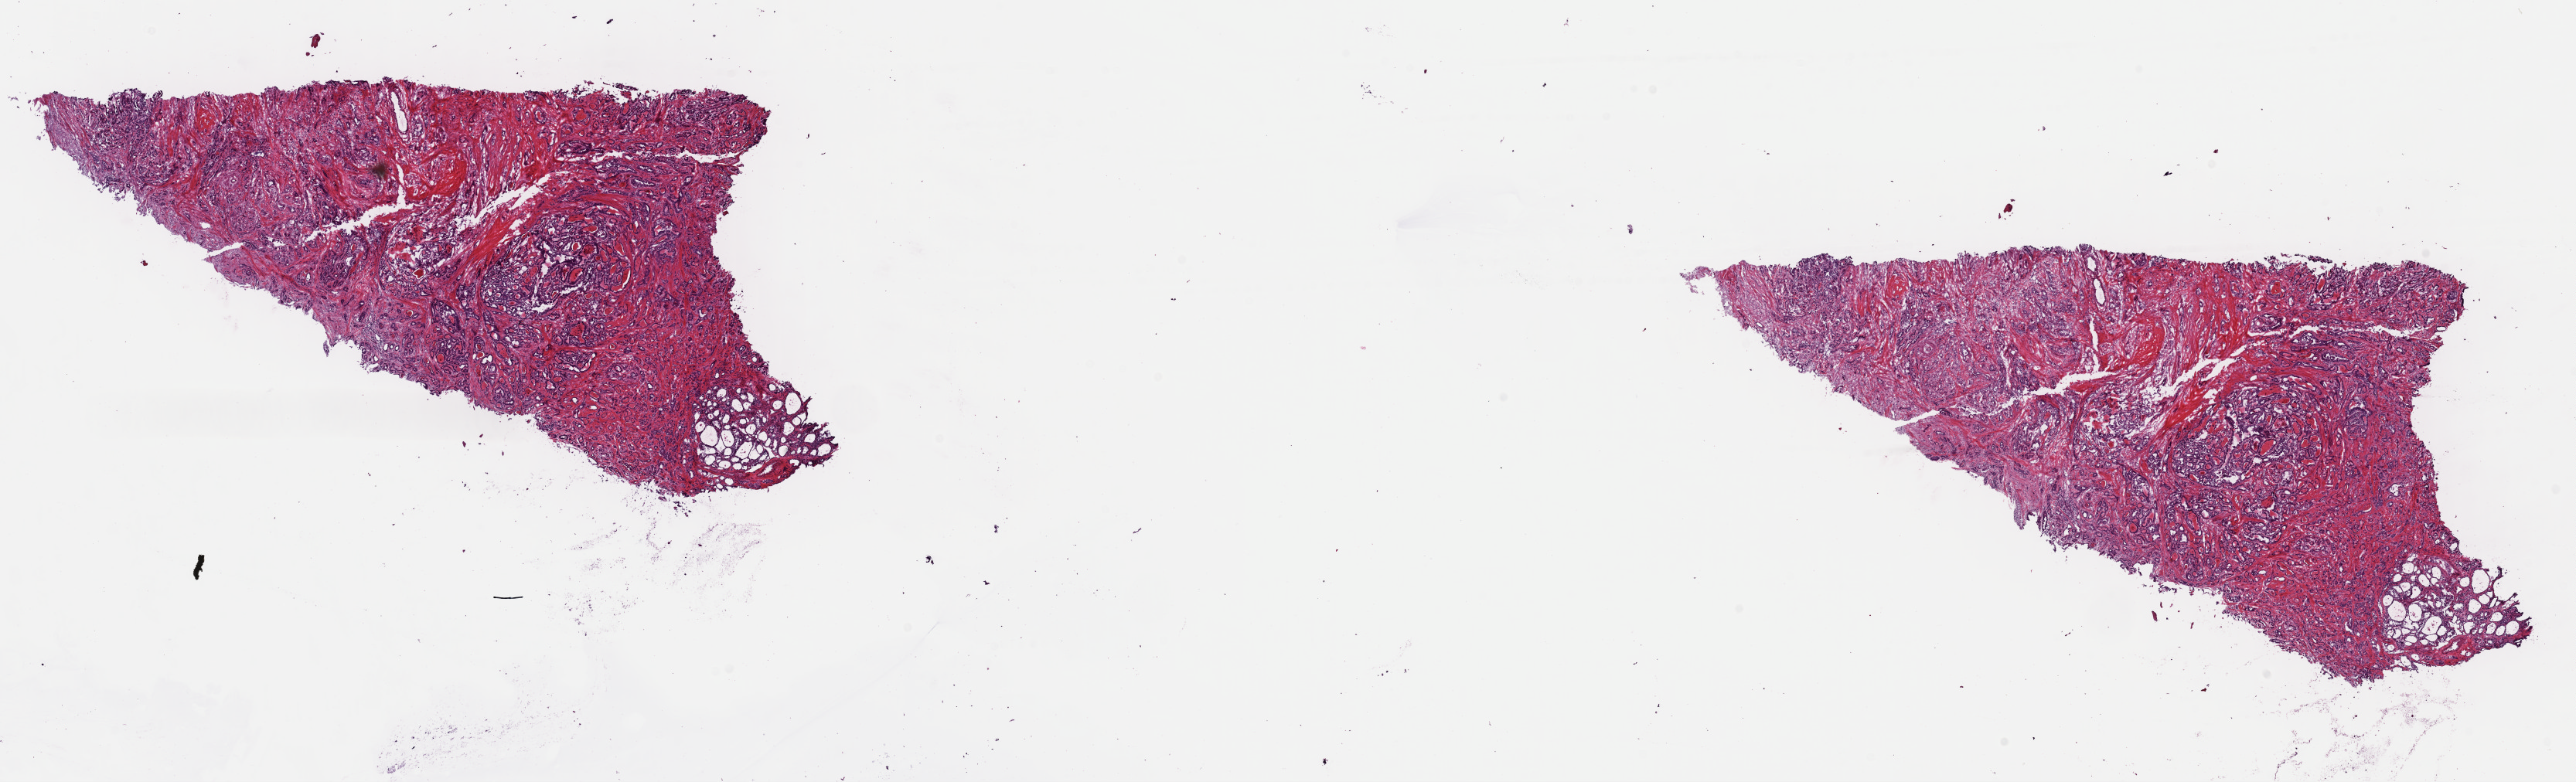
Hematoxylin and eosin (H&E) stained whole-slide image, shown as a low-resolution overview of the whole scanned area (about 26.3 x 8.0 mm, acquisition: 40x scan); frozen section from the top of the tissue portion; thyroid, primary tumour sample. Female patient; age at initial diagnosis 56 years. Slide review estimates, as recorded: tumour cells 95%, tumour nuclei 70%, normal cells 5%, stromal cells 0%, necrosis 0%. Inflammatory infiltration, as recorded: lymphocyte infiltration 0%, monocyte infiltration 0%, neutrophil infiltration 0%.
Lymph nodes positive (case pathology): 0 of 1 examined. AJCC pathologic stage: III (7th edition). Pathologic diagnosis: Papillary adenocarcinoma, NOS (thyroid gland).